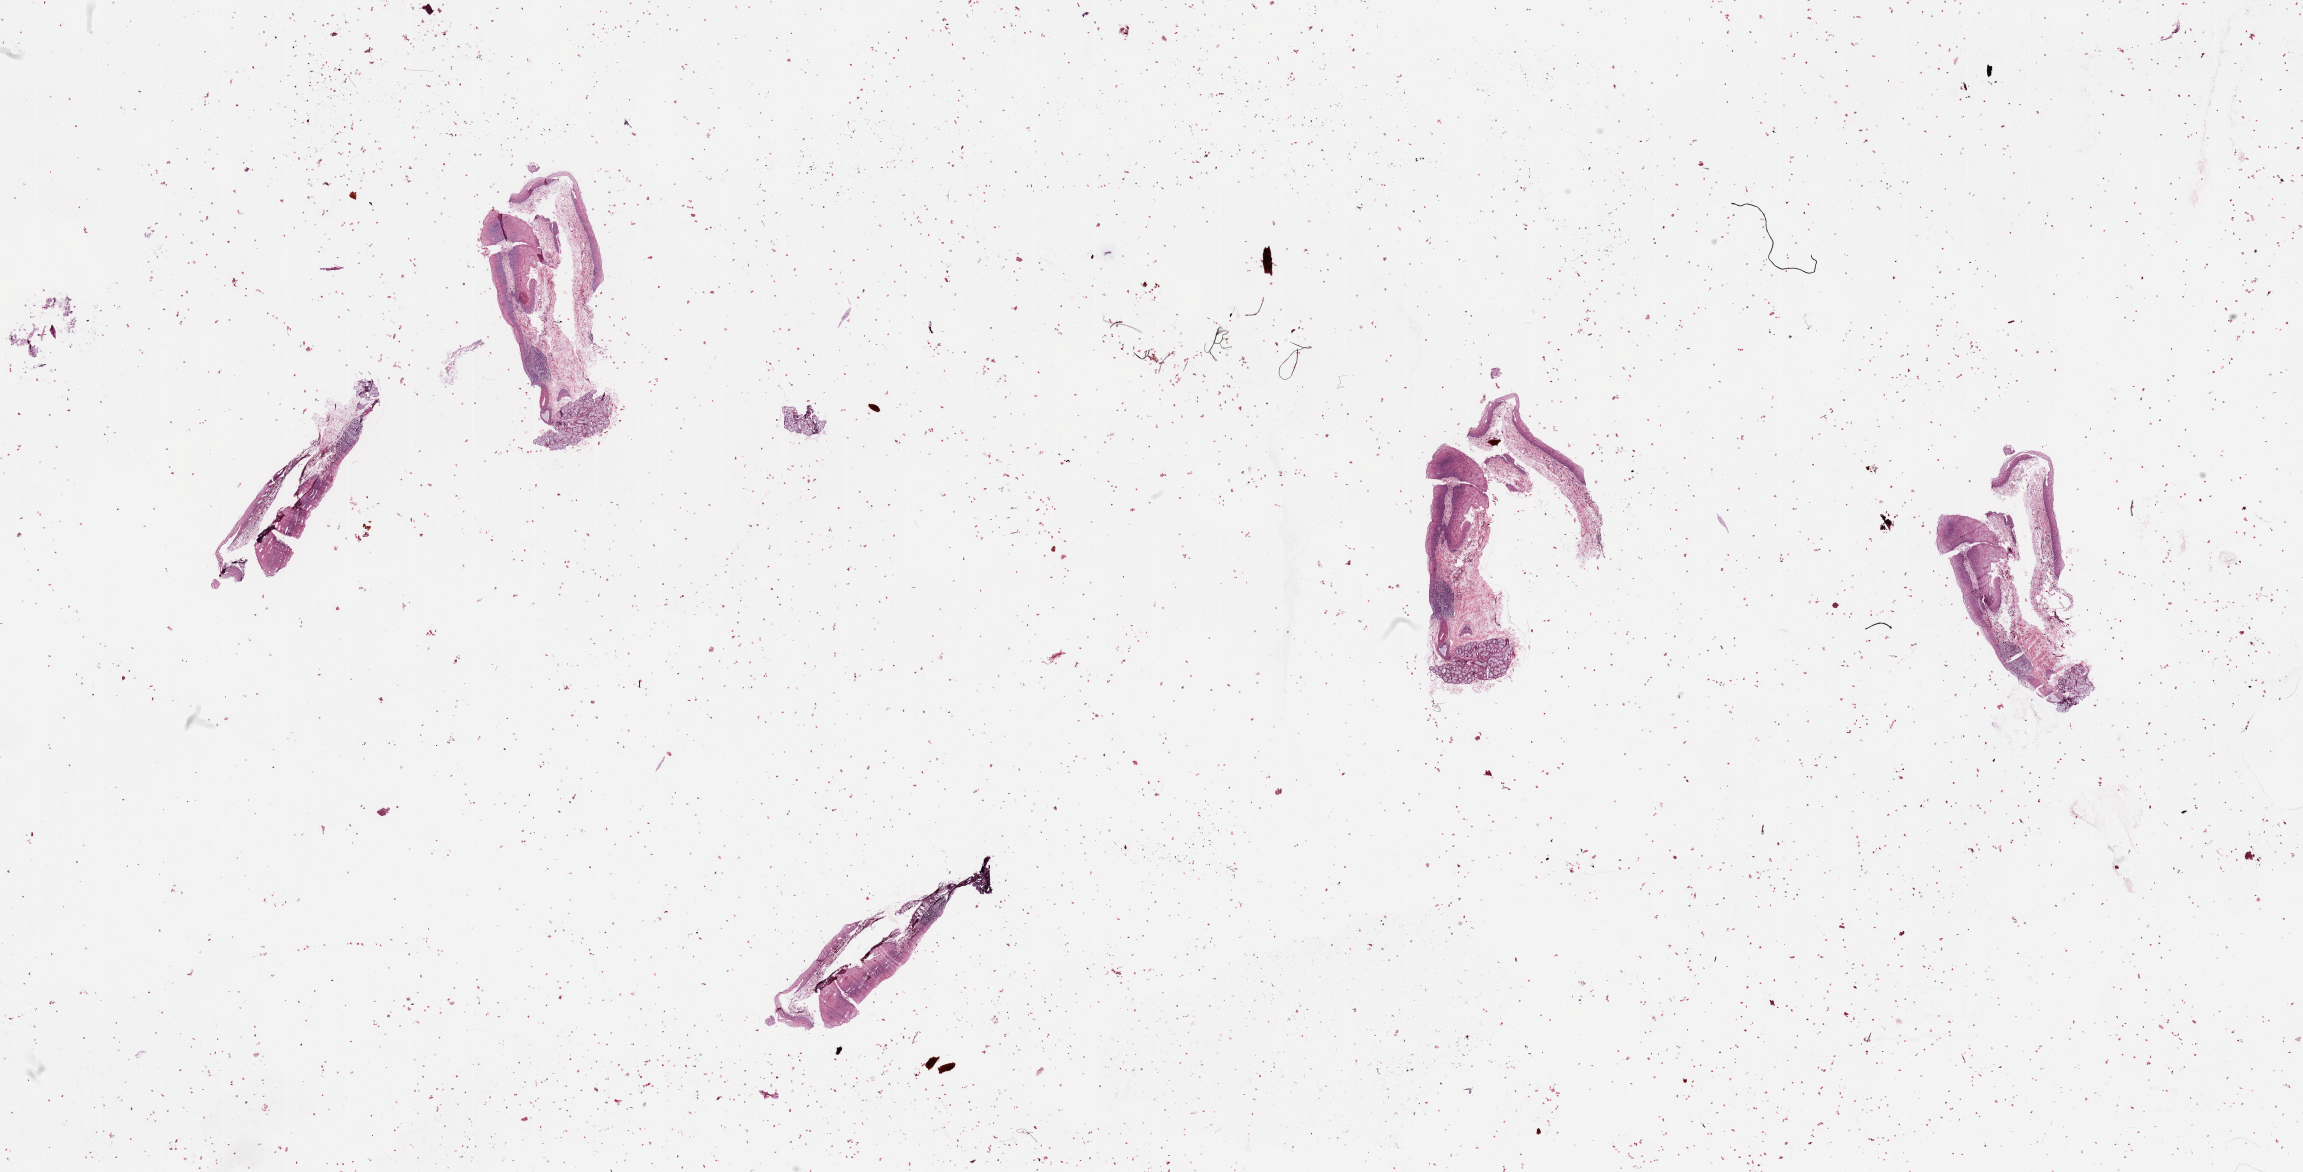
Digitized Hematoxylin and eosin (H&E) stained tissue section (whole slide), shown as a low-resolution overview of the whole scanned area (about 36.4 x 18.5 mm); normal (non-tumour) tissue sample, sampled site: larynx. 71-year-old male patient.
This section: normal (non-tumour) tissue from the same patient. Patient diagnosis: Squamous cell carcinoma, NOS (larynx, NOS).